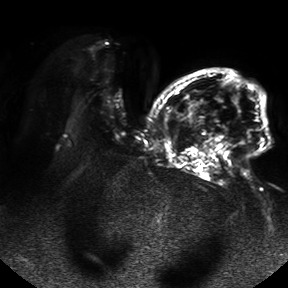
Breast MRI, one axial slice; diffusion-weighted series; image 2 of 4 stored at this slice position (different b-values; order by instance number); 1.5 T; 288 × 288 image matrix, field of view 390 × 390 mm. Female patient.
Annotated regions visible in this slice (expert manual segmentation):
- tumour on diffusion-weighted imaging: box from (x=176, y=95) to (x=238, y=122) px